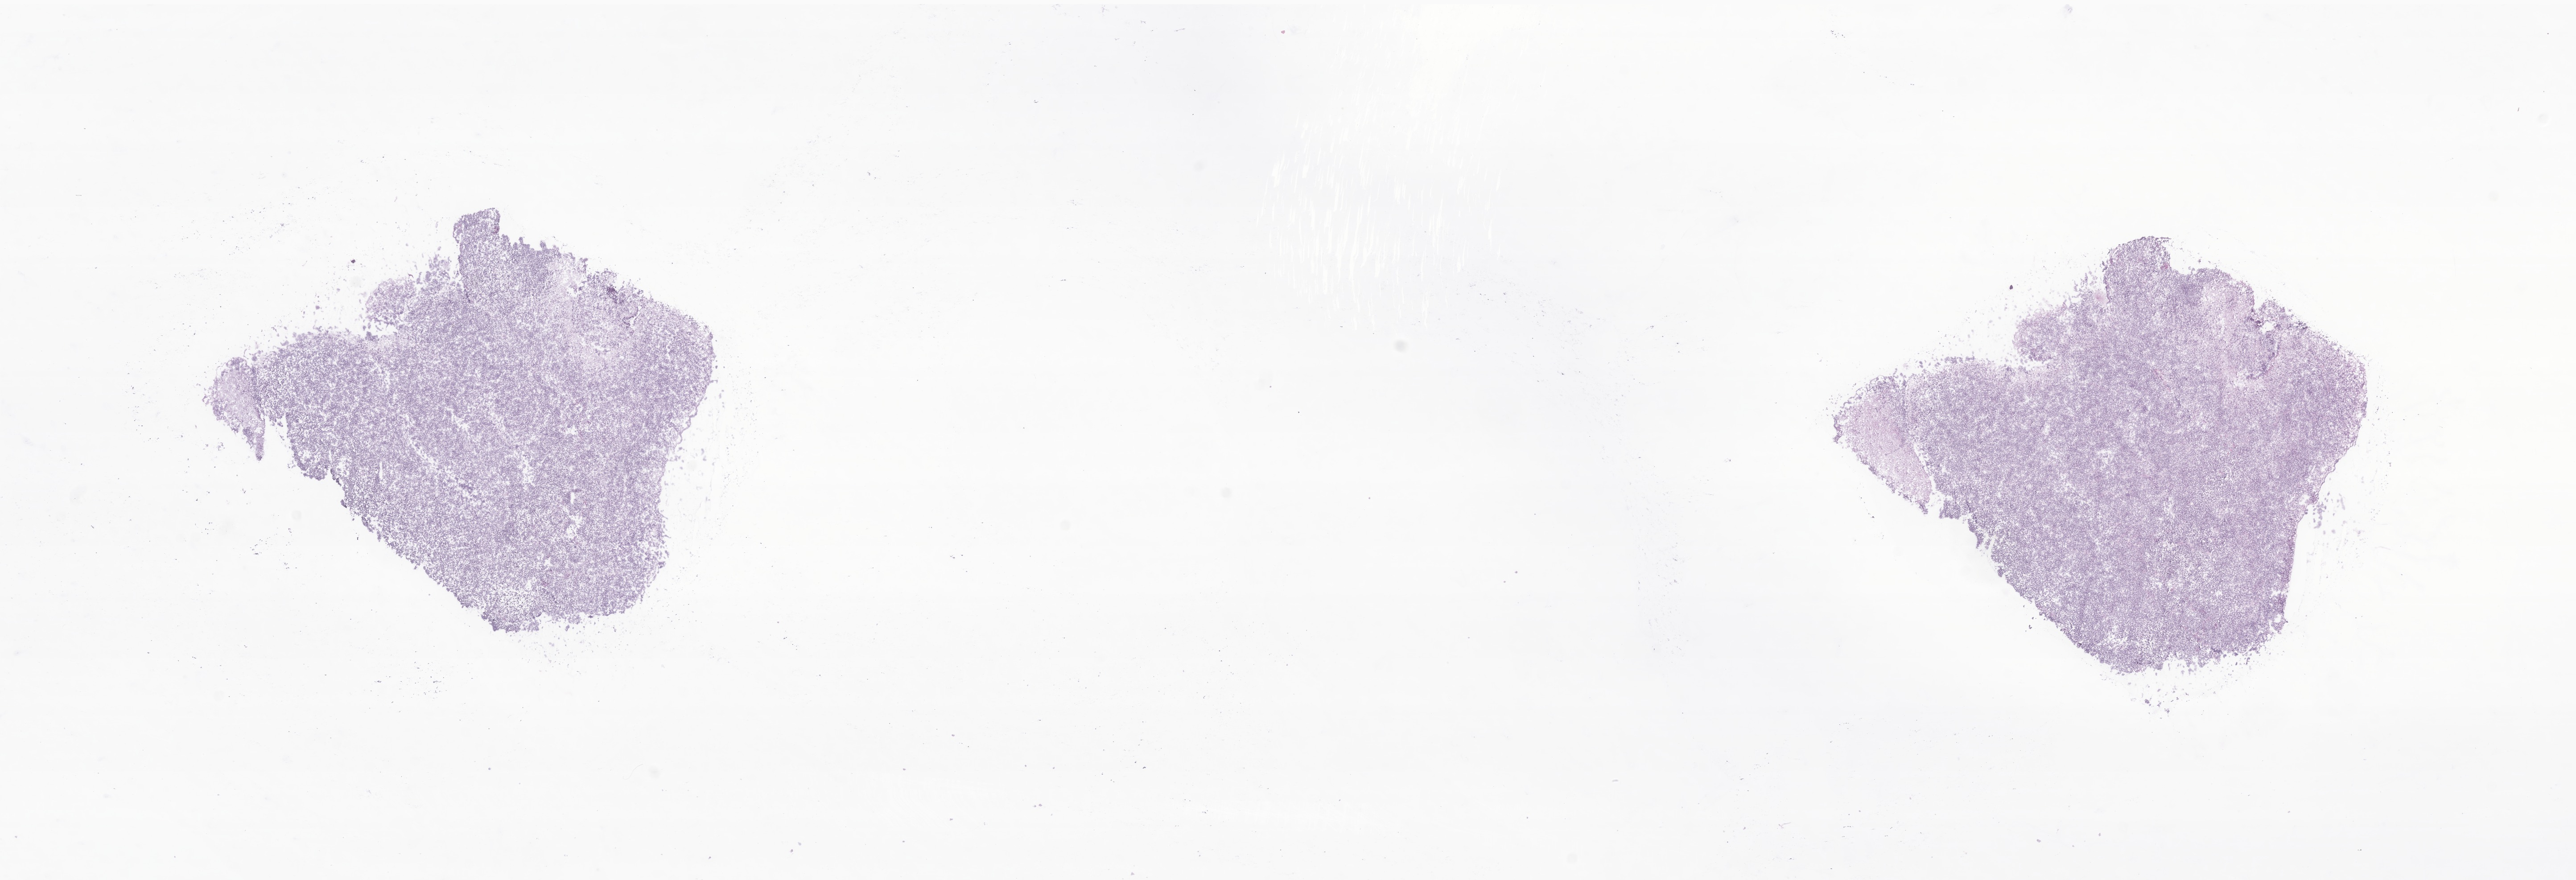
H&E whole-slide image of tumor tissue from the brain, a low-resolution overview of the entire scanned area, about 24.4 x 8.3 mm, frozen section (OCT-embedded). Male patient, age 162 months (13 years 6 months).
* recorded diagnosis: Medulloblastoma, NOS